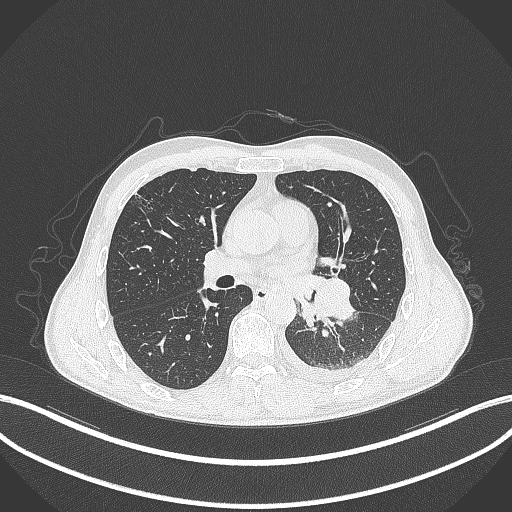
Chest CT, one axial slice. Position 172 of 295 along the scan axis. Reconstruction kernel B70f. 120 kVp. Lung window (W 1500 / L -600 HU). 1 mm slice thickness. 512 × 512 image matrix, field of view 400 × 400 mm. Patient: male, 47 years. Case-level facts recorded for this patient, not image findings: clinical TNM (as recorded): T3 N1 M1c; histopathological grade: G3.
Structures marked on this image (bounding box drawn by a radiologist):
- lung tumour (recorded histology: small cell carcinoma): bounding box <311,275,354,326> (left, top, right, bottom; pixels)